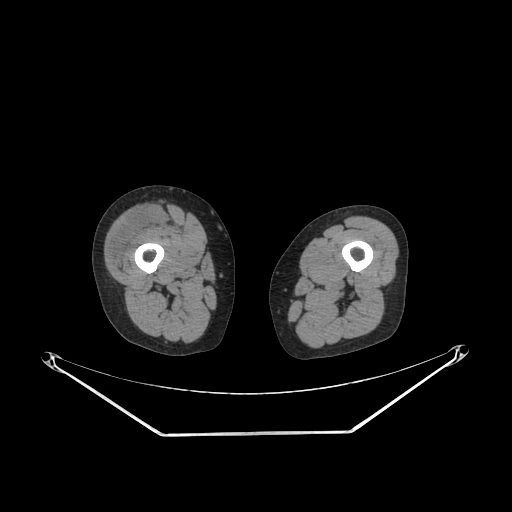
CT of an extremity soft-tissue mass (from a PET/CT study), one axial slice; slice 217 of 311 in the series (ordered by position); reconstruction kernel SOFT; 140 kVp; soft-tissue window (W 400 / L 40 HU); 3.75 mm slice thickness; 512 × 512 image matrix, field of view 500 × 500 mm. Female patient. Case-level facts recorded for this patient, not image findings: histological type: pleiomorphic undifferentiated sarcoma; grade: high; site of the primary tumour: right quadricep.
Structures marked on this image (expert contour drawn on MRI and transferred to this co-registered scan by the dataset authors):
- tumour plus oedema (research contour): bounding box [x1, y1, x2, y2] px = [107, 208, 163, 270]